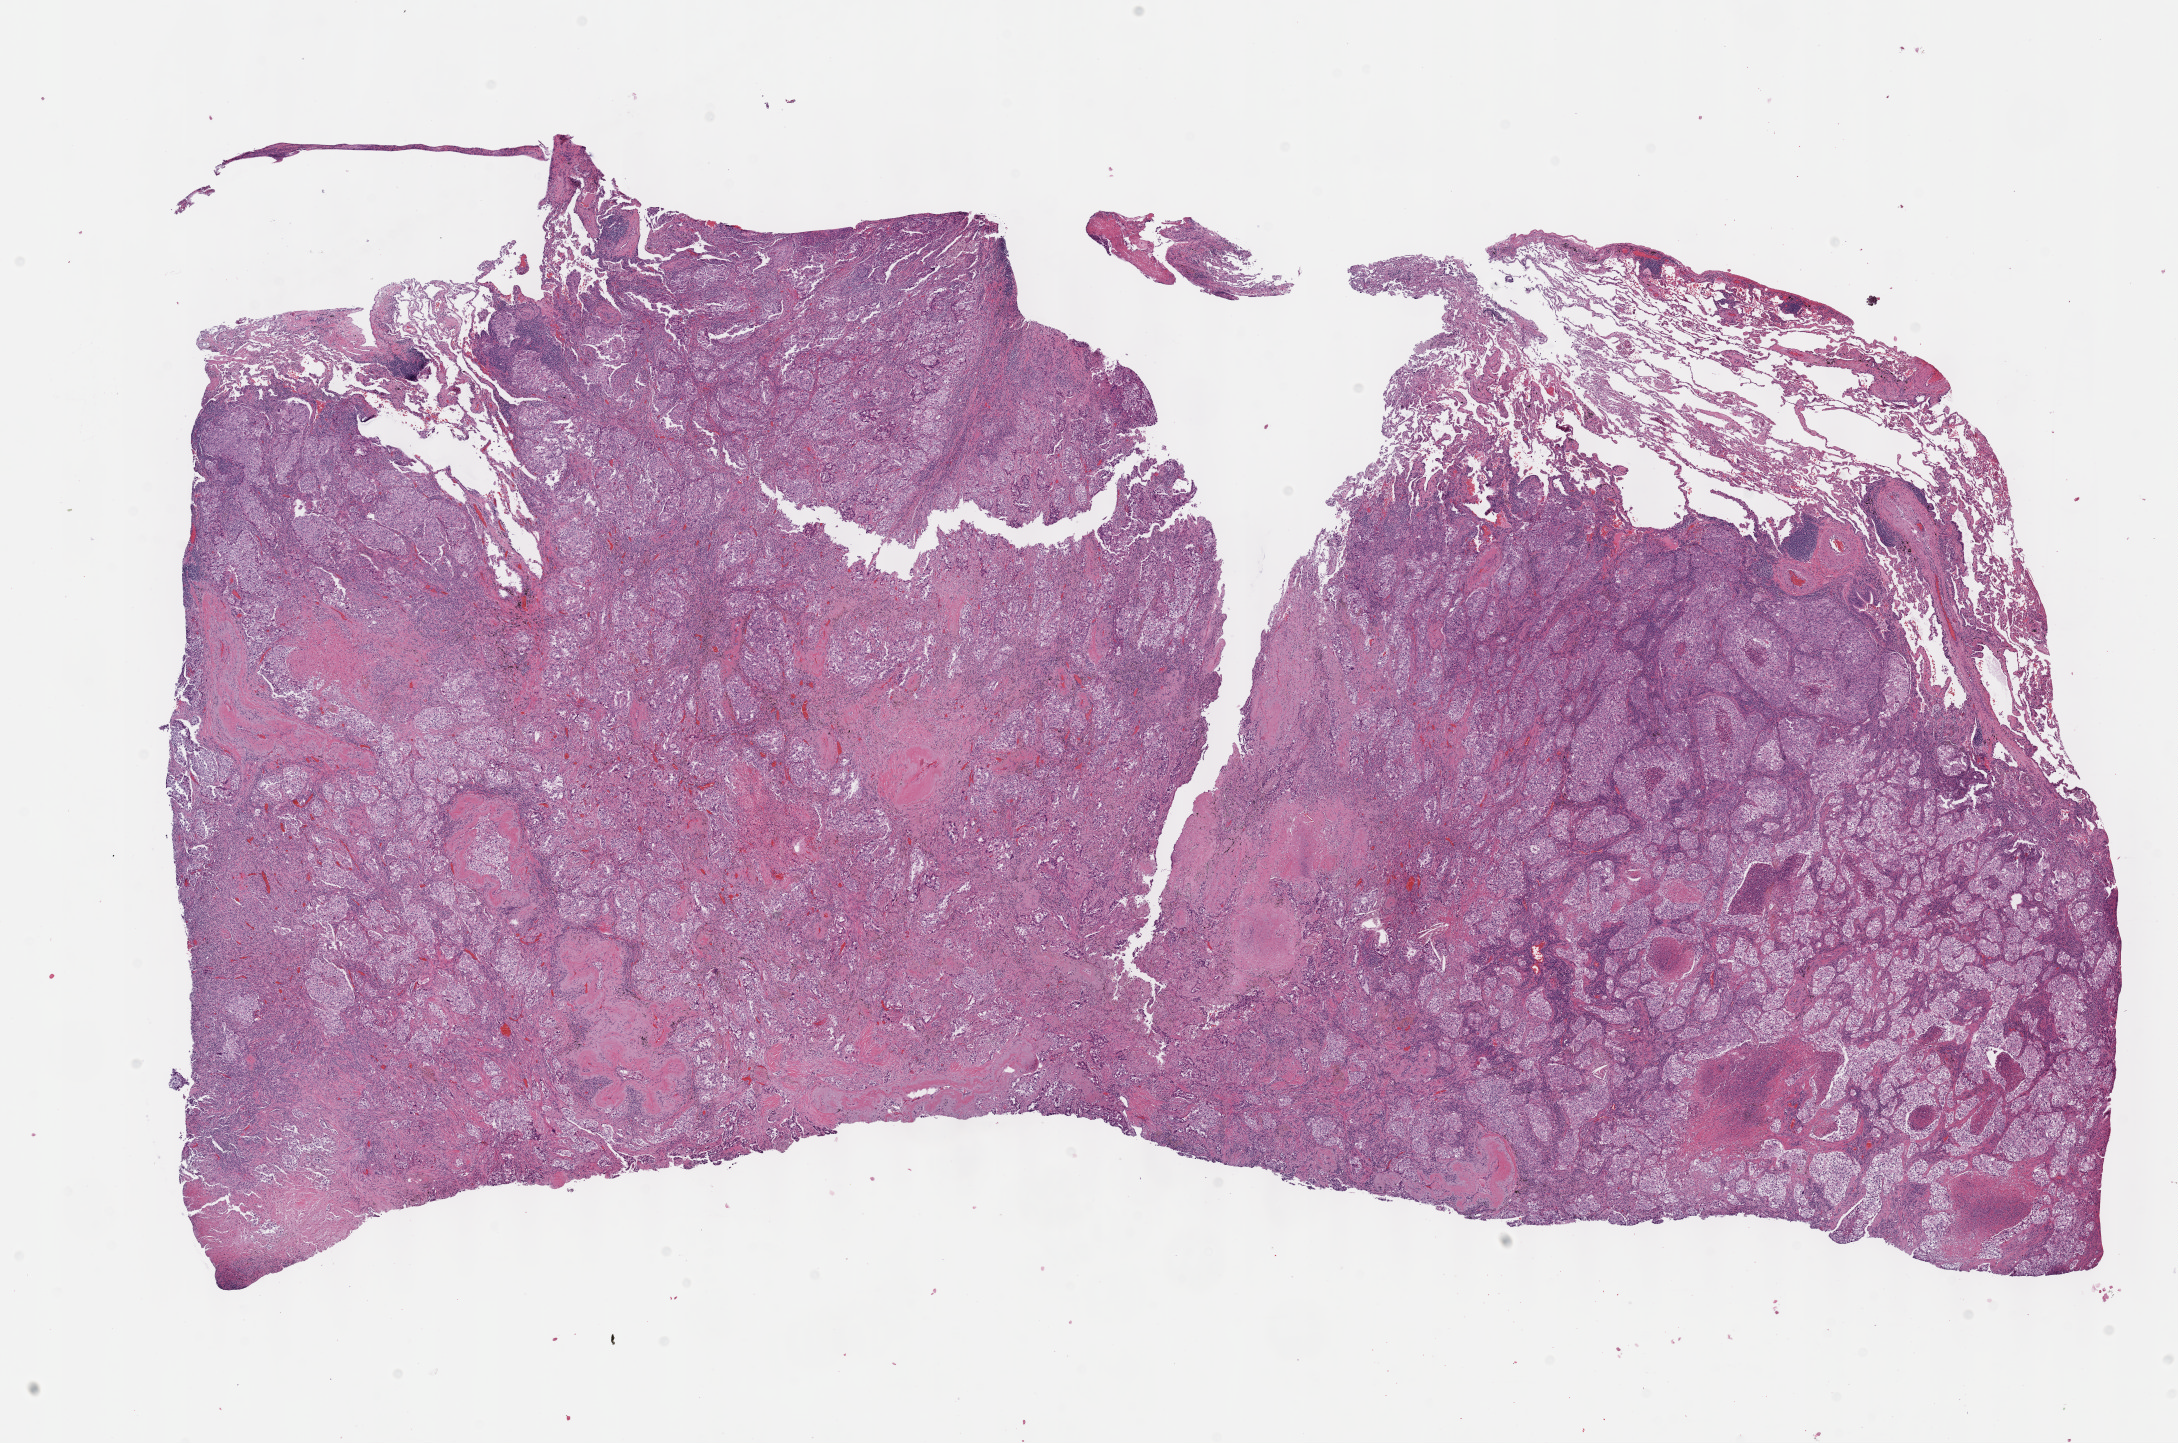
Whole-slide histology image, H&E-stained — low-resolution overview of the scanned area, about 17.6 x 11.7 mm. Formalin-fixed paraffin-embedded (FFPE) diagnostic section. Lung, primary tumour sample. Female patient; age at initial diagnosis 68 years.
Histologic diagnosis: Adenocarcinoma, NOS (lower lobe, lung).